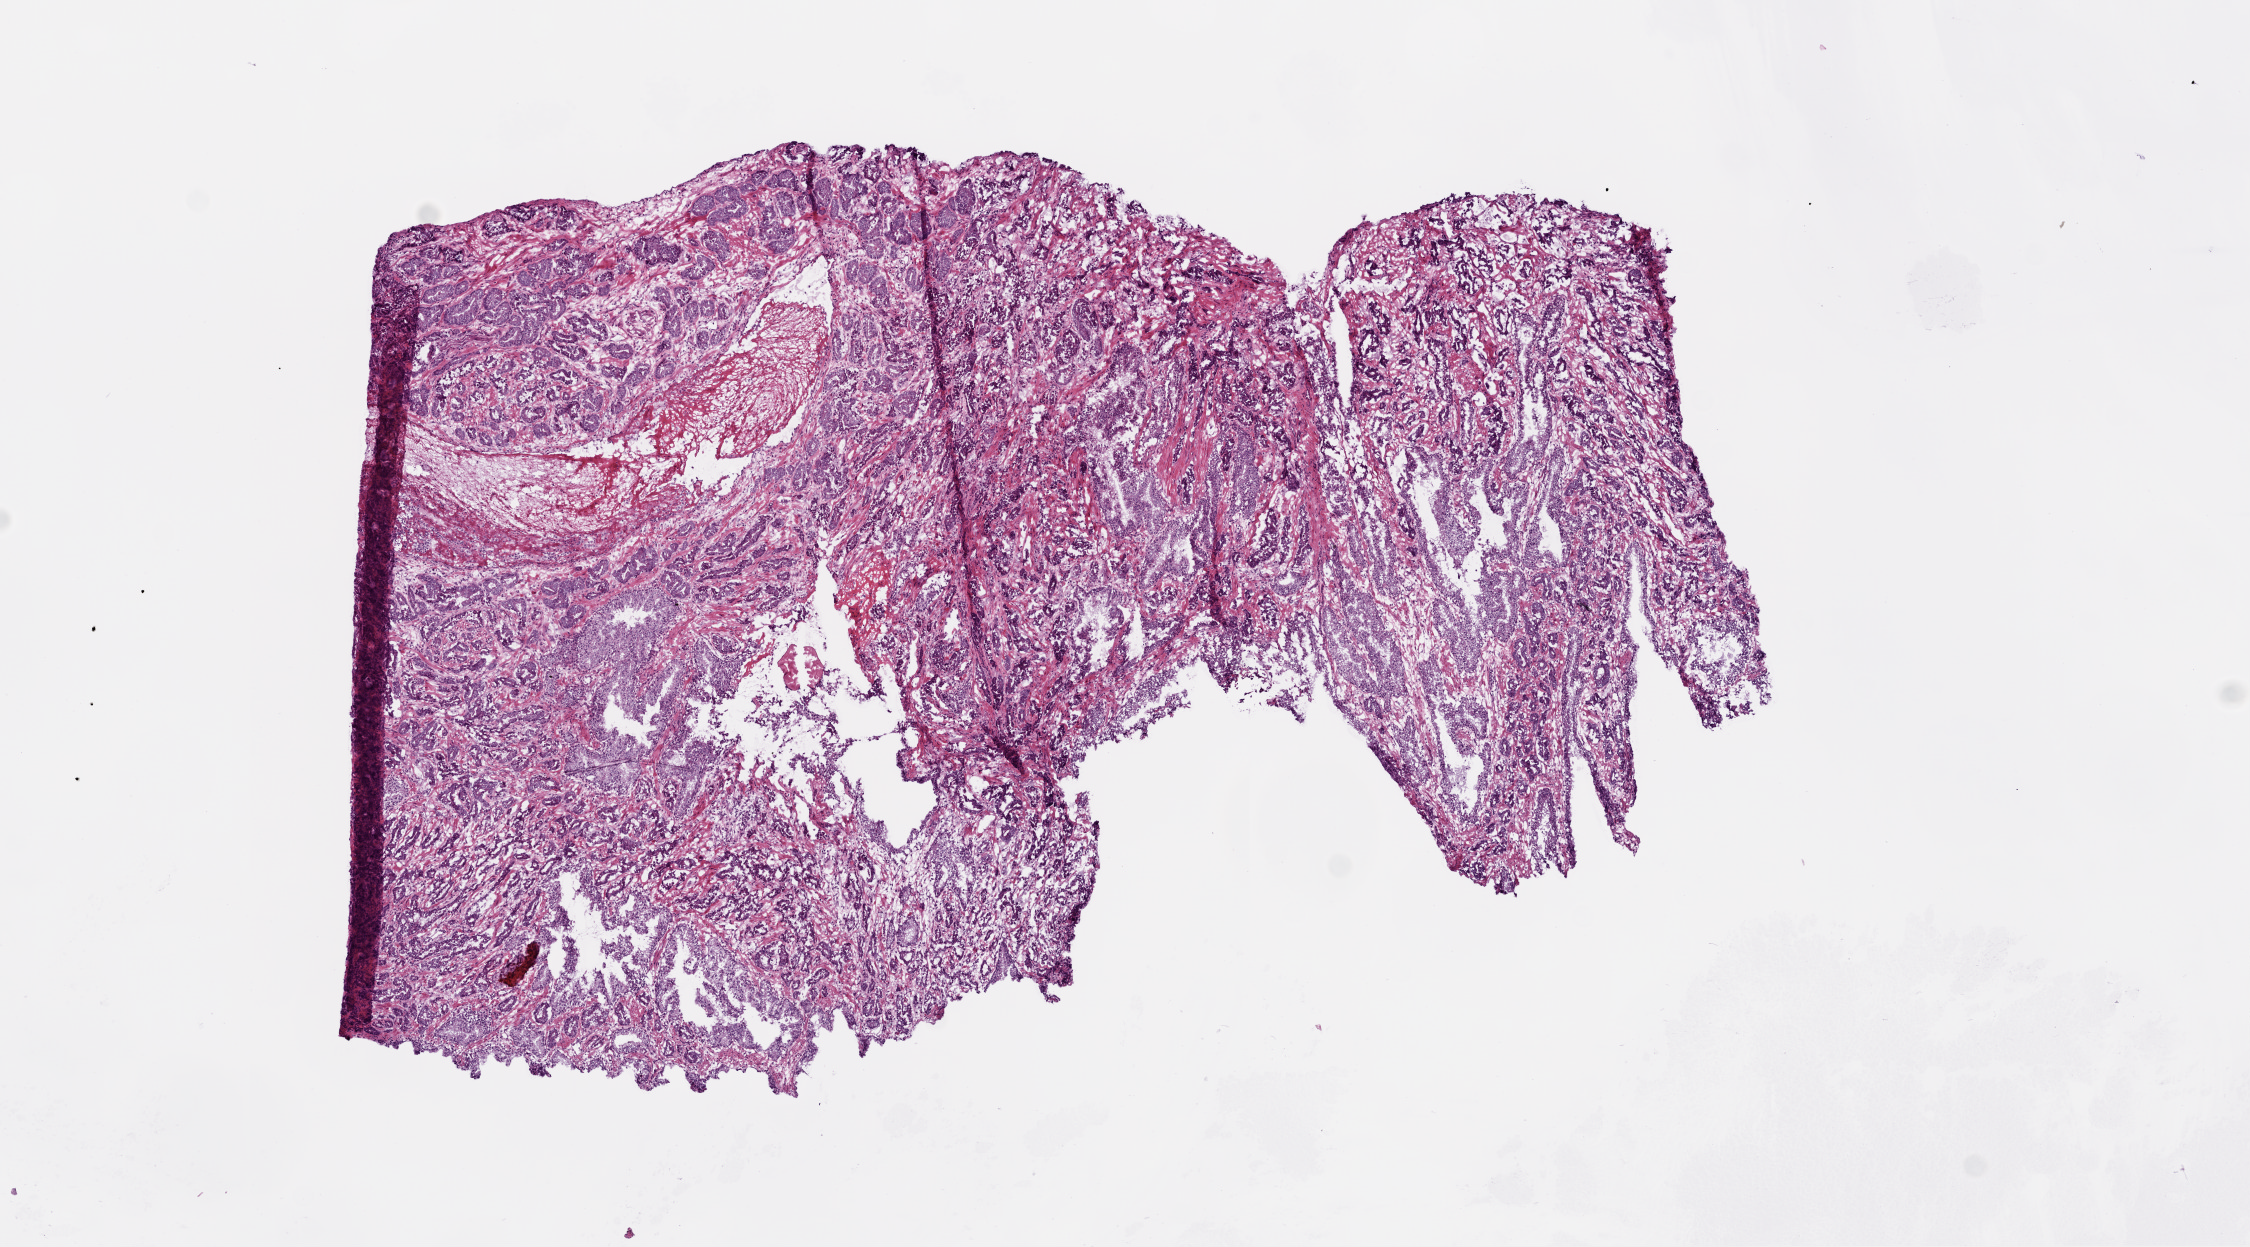
H&E-stained whole-slide image — shown as a low-resolution overview of the whole scanned area (about 9.0 x 5.0 mm), frozen section from the bottom of the tissue portion, primary tumour sample from the prostate. Male patient; age at initial diagnosis 55 years. Gleason score: 7 (3+4). Slide review estimates, as recorded: tumour cells 60%, tumour nuclei 70%, normal cells 25%, stromal cells 13%, necrosis 2%. Inflammatory infiltration, as recorded: lymphocyte infiltration 2%, monocyte infiltration 2%, neutrophil infiltration 0%.
• lymph nodes positive (case pathology): 0 of 7 examined
• diagnosis: Acinar cell carcinoma (prostate gland)